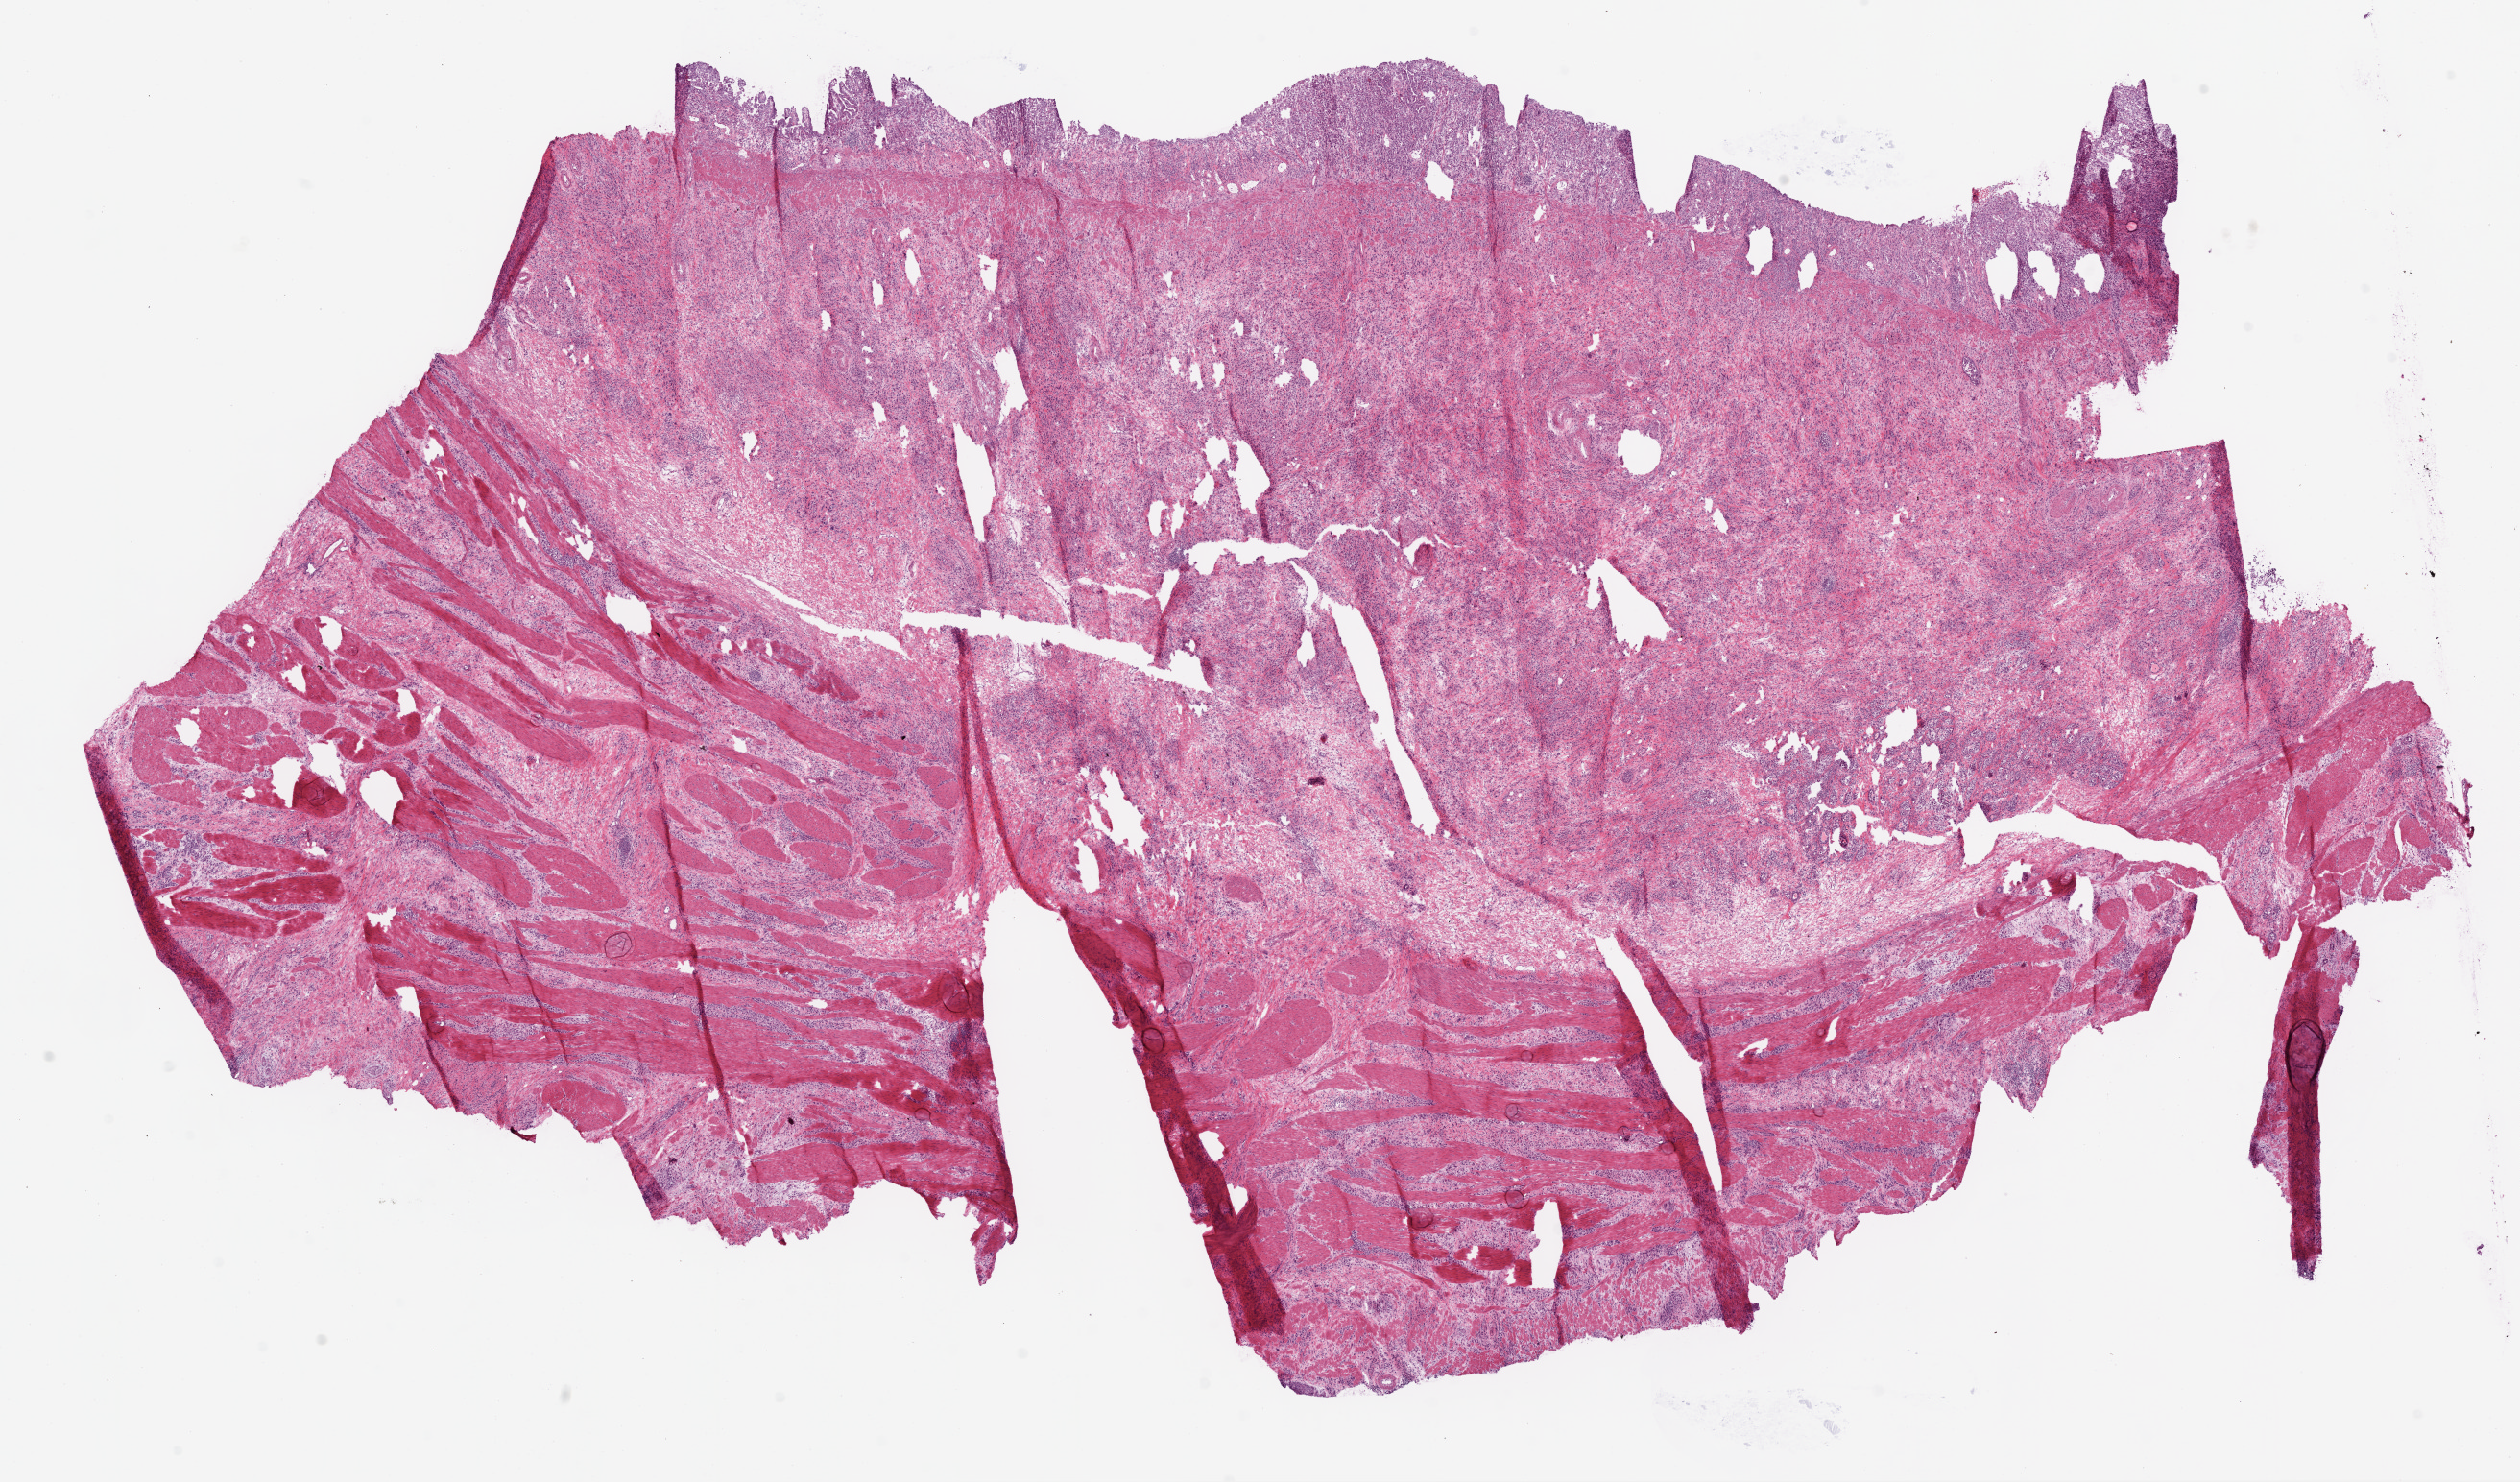
Digitized Hematoxylin and eosin (H&E) stained tissue section (whole slide) — a low-resolution overview of the entire scanned area, about 21.1 x 12.4 mm (slide scanned at 20x); frozen section; sample: primary tumour, stomach. Female patient; age at initial diagnosis 76 years. Histologic grade: G3 (poorly differentiated). Slide review estimates, as recorded: tumour cells 79%, tumour nuclei 75%, normal cells 1%, stromal cells 20%, necrosis 0%.
Histologic diagnosis: Adenocarcinoma, NOS. AJCC pathologic stage: IIIA (6th edition).